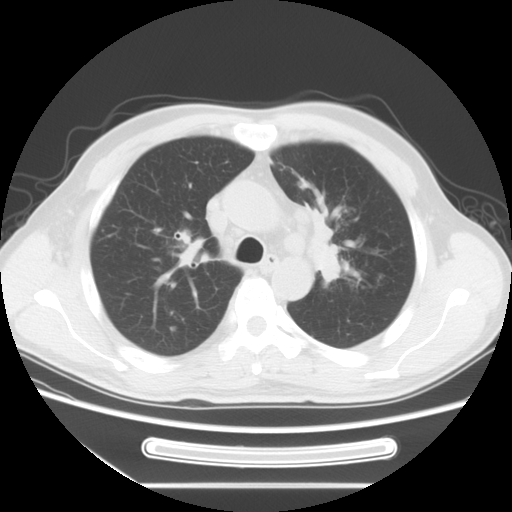
Chest CT, one axial slice; slice 50 of 71 in the series (ordered by position); reconstruction kernel STANDARD; 120 kVp; lung window (W 1500 / L -600 HU); 512 × 512 image matrix, field of view 366 × 366 mm. Patient: male, 51 years. From the clinical record (not read from this slice): clinical TNM (as recorded): T1c N3 M0.
Outlined on this slice (bounding box drawn by a radiologist):
- lung tumour (recorded histology: adenocarcinoma): box from (x=302, y=196) to (x=353, y=301) px